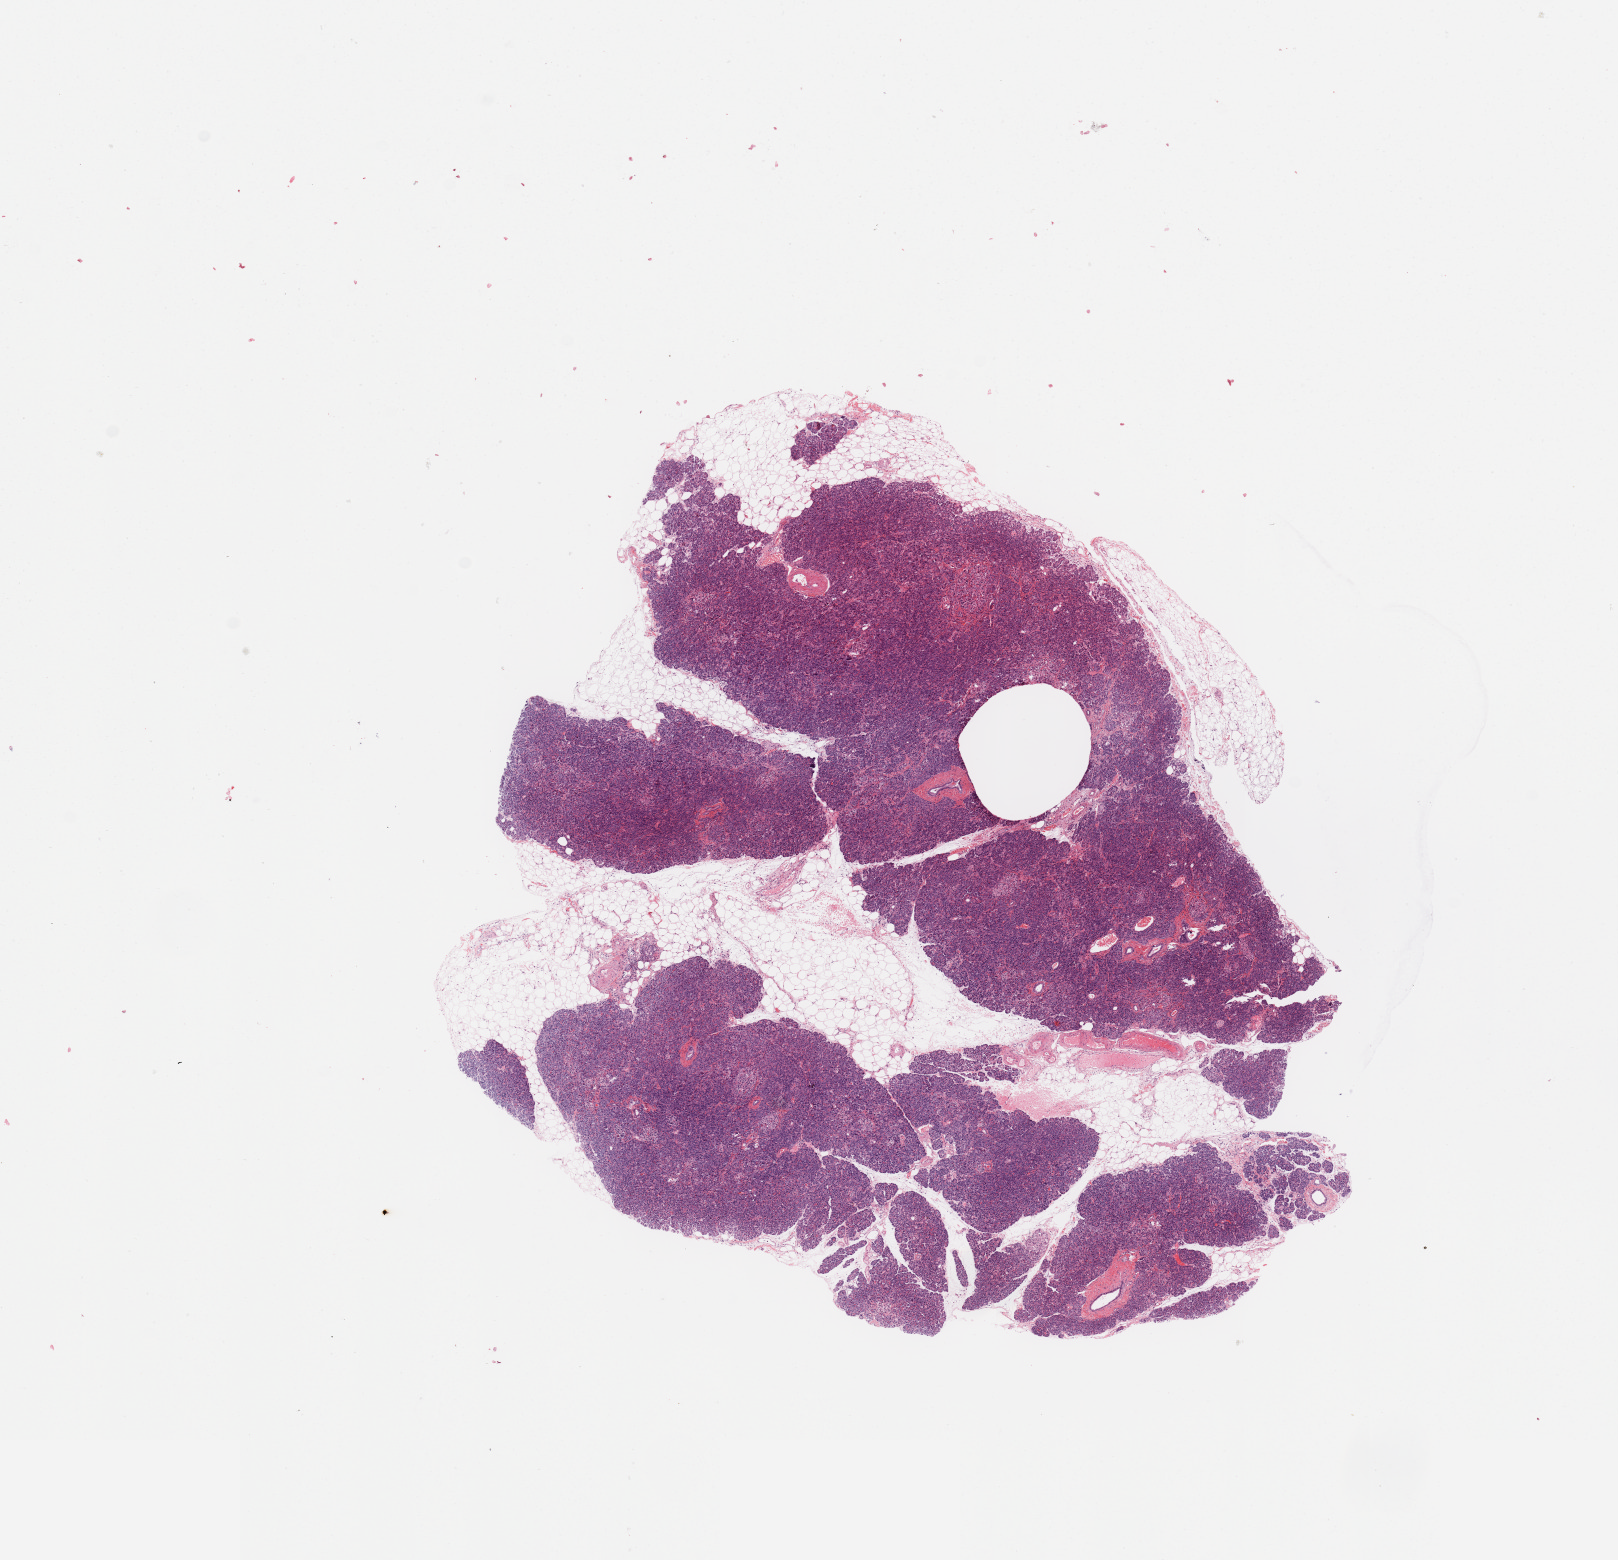
H&E-stained whole-slide image — a low-resolution overview of the entire scanned area, about 12.8 x 12.3 mm; pancreas, normal (non-tumour) tissue. Male, 73 y/o.
- this section: normal (non-tumour) tissue from the same patient
- patient diagnosis (cohort enrolment): ductal adenocarcinoma (pancreas)